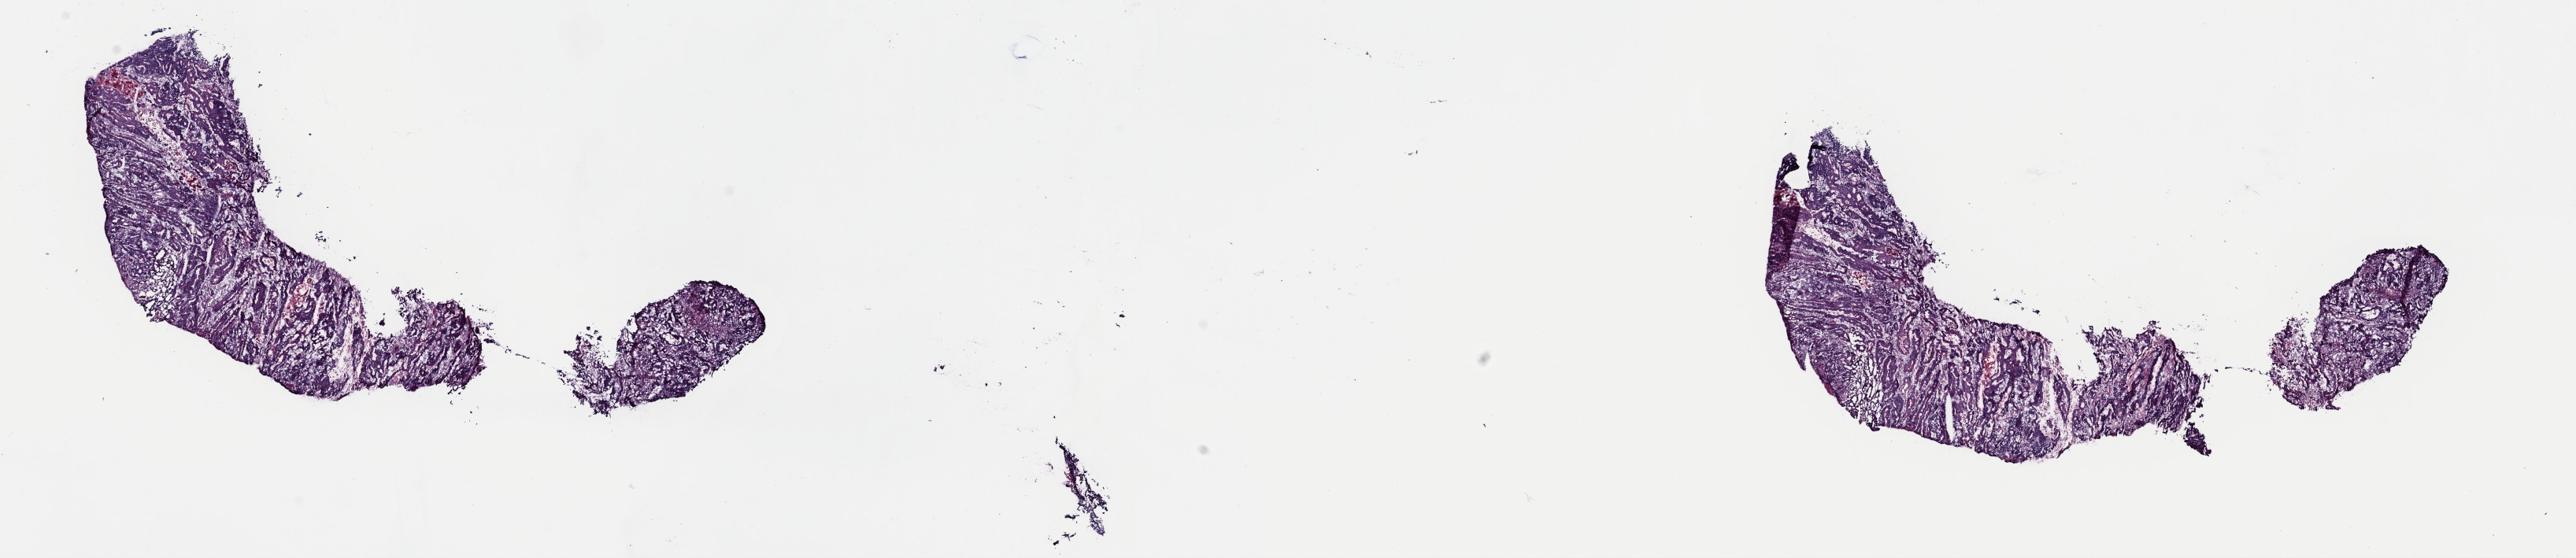
Digitized Hematoxylin and eosin (H&E) stained tissue section (whole slide) — a low-resolution overview of the entire scanned area, about 25.8 x 5.6 mm, frozen section from the top of the tissue portion, sample: primary tumour, stomach. Female, age 71 years at initial diagnosis. Composition of this section per pathologist review: tumour cells 70%, tumour nuclei 80%.
Pathologic diagnosis: Tubular adenocarcinoma (gastric antrum).